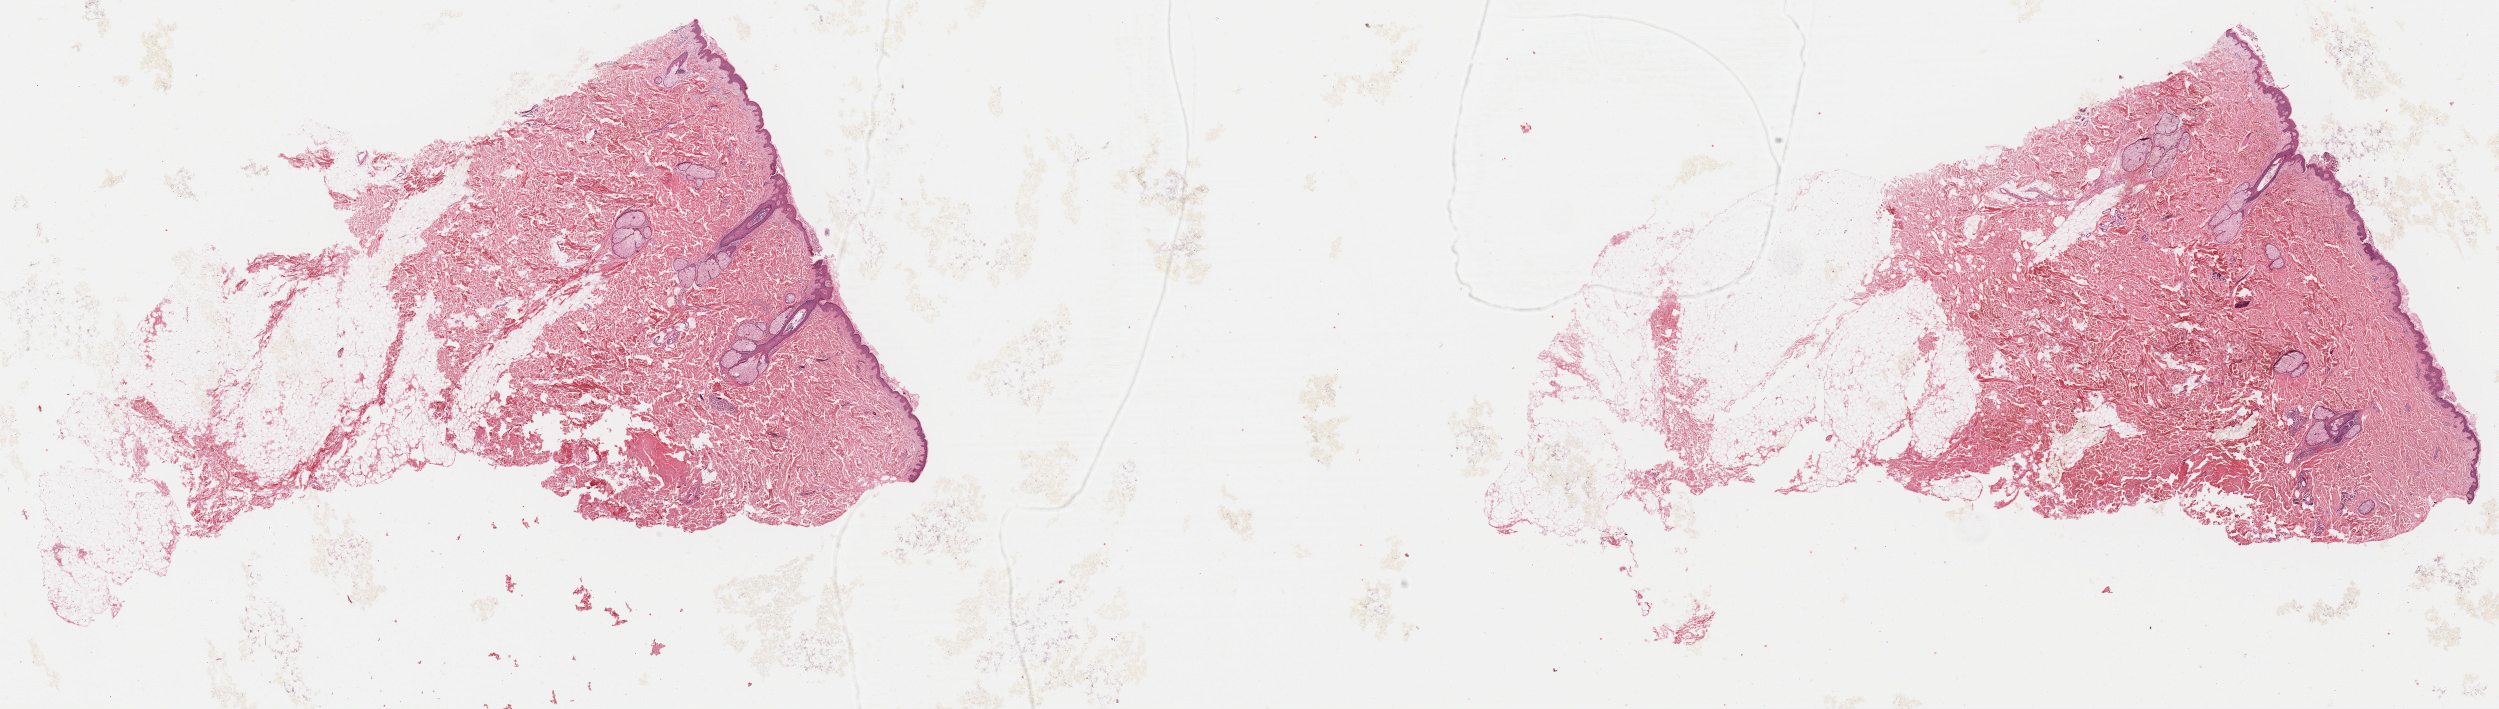
Whole-slide histology image, H&E — a low-resolution overview of the entire scanned area, about 39.3 x 11.1 mm (slide scanned at 40x). FFPE section. Skin, primary tumour sample. Patient: male, age at initial diagnosis 43 years.
* AJCC pathologic stage: IIIA (5th edition)
* diagnosis: Malignant melanoma, NOS
* TNM: T4b N1a M0